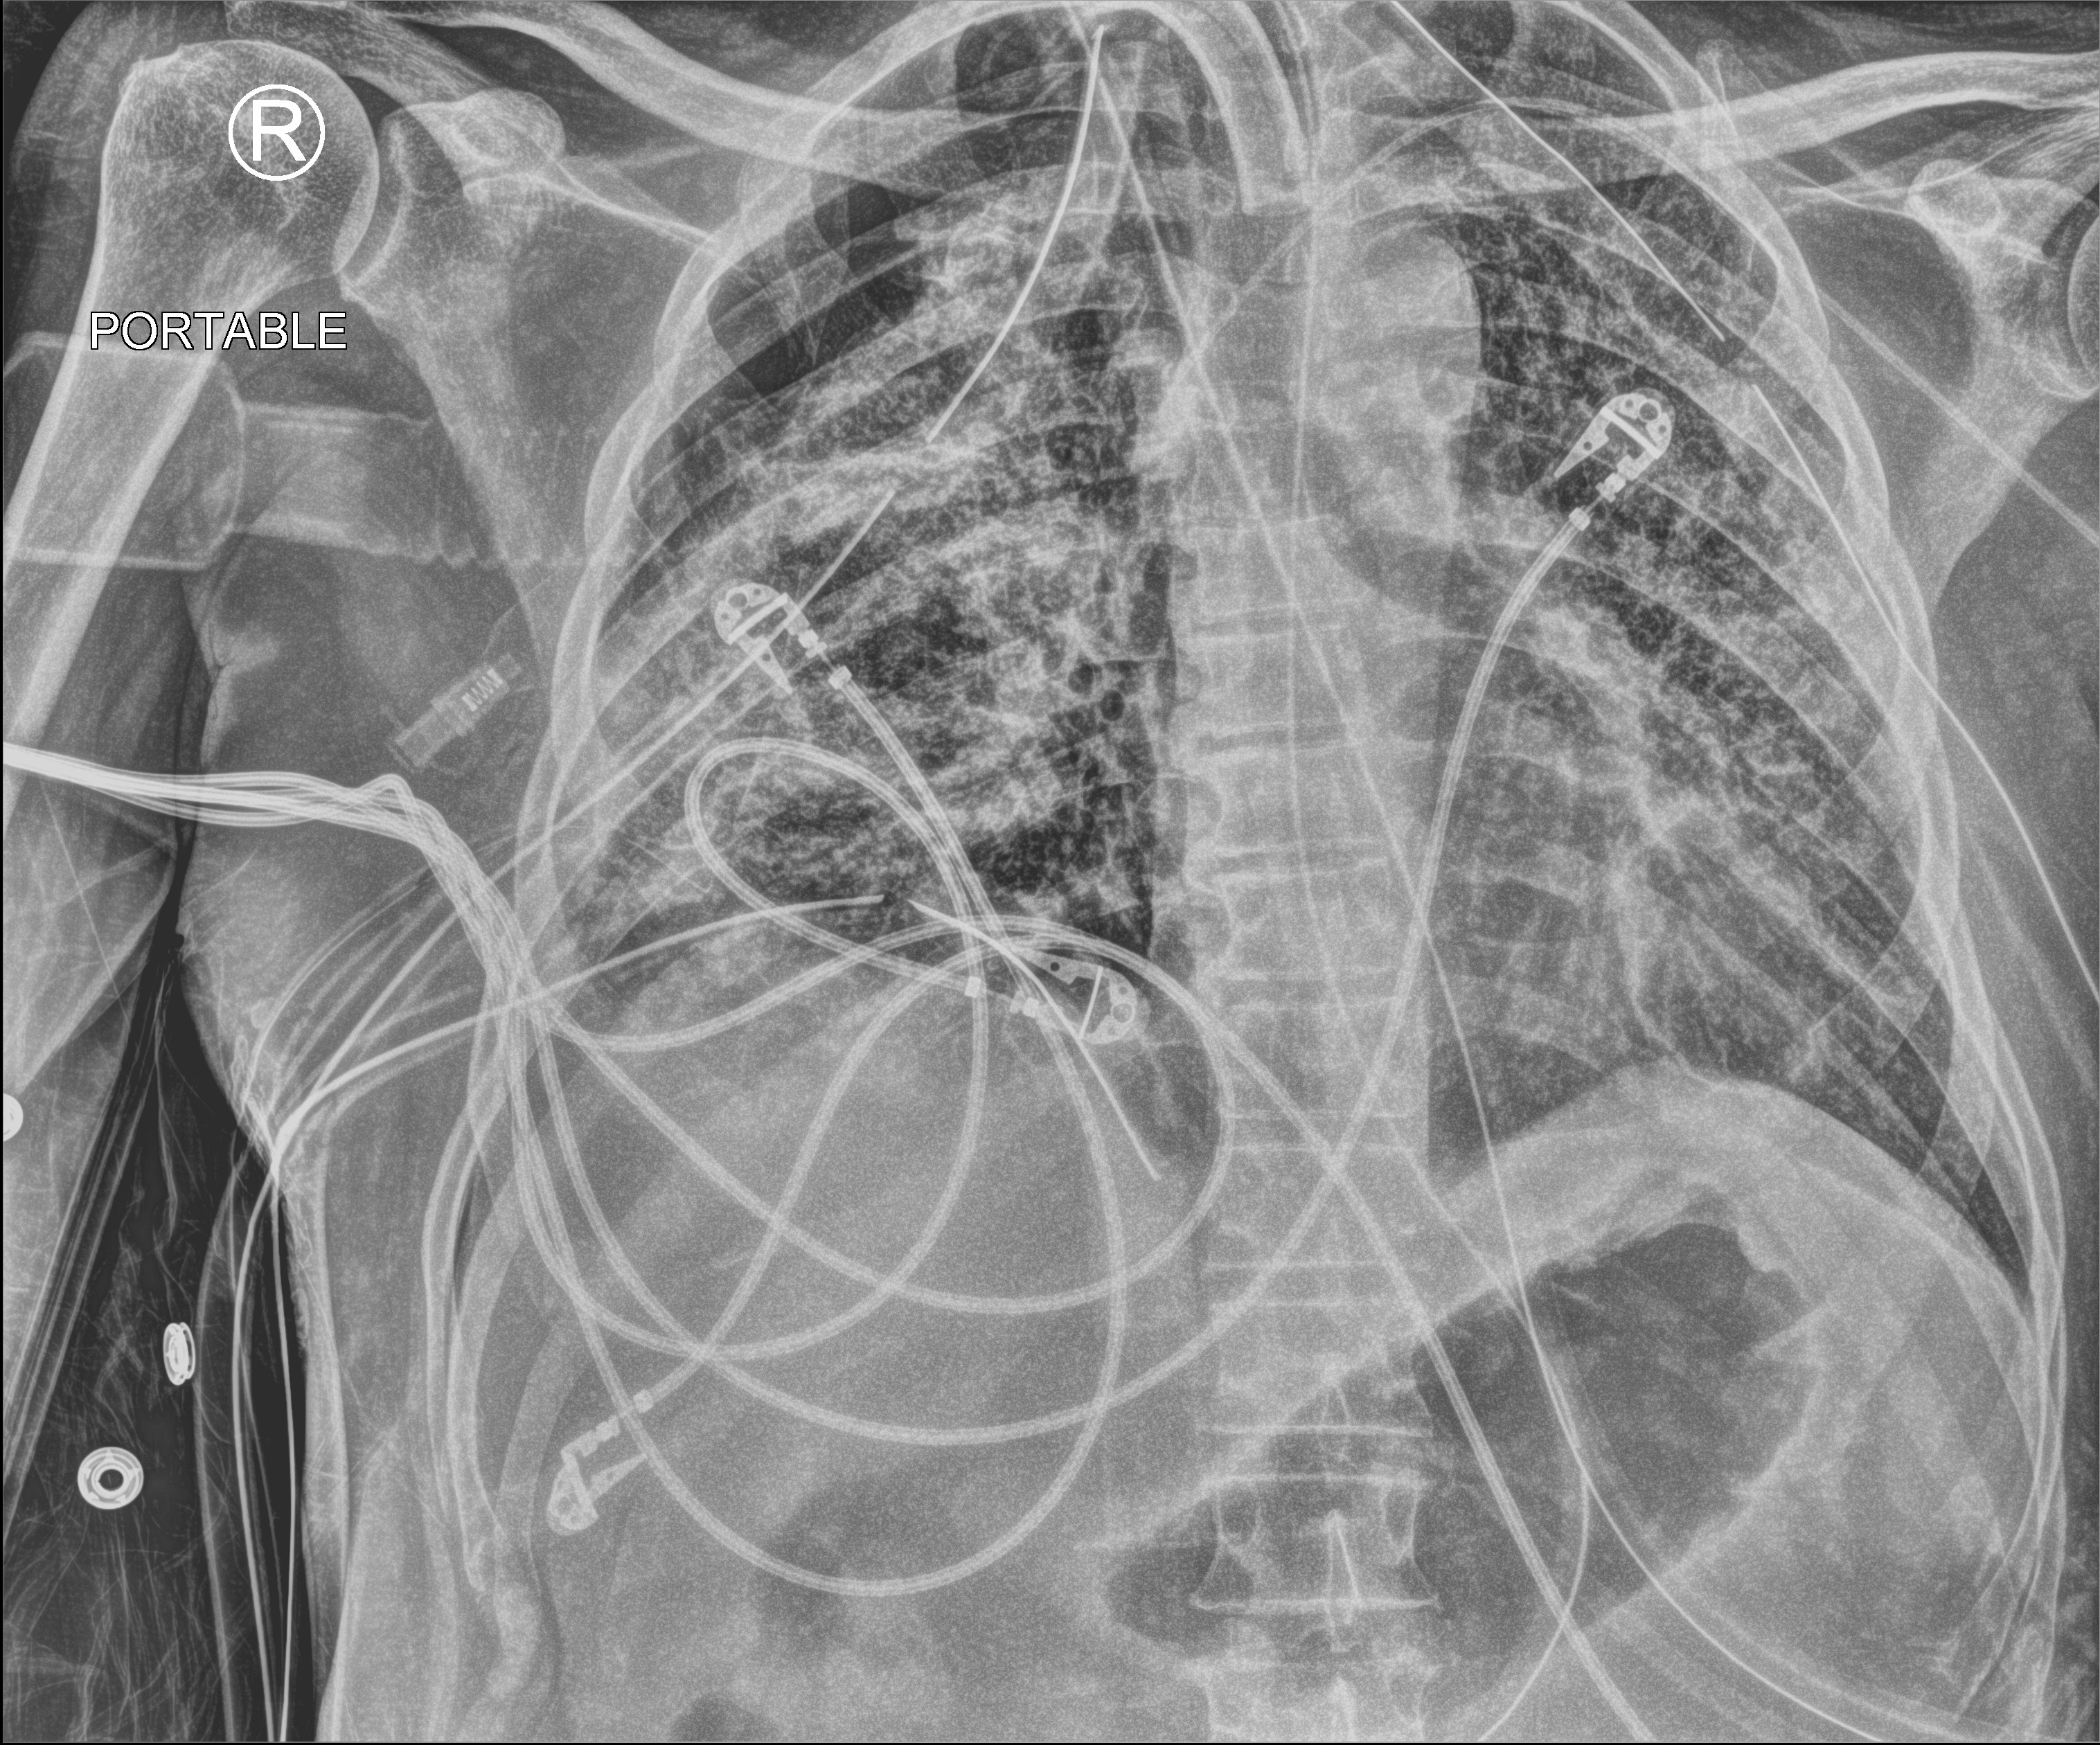
Portable chest radiograph, anteroposterior (AP) projection. Male patient hospitalised with COVID-19, age 18–59 years.
Hospital-stay facts (about this admission, not read from this image; timing relative to this image not recorded): mechanically ventilated during this hospital stay: yes; admitted to intensive care during this hospital stay: yes; hypertension (admission record): yes.